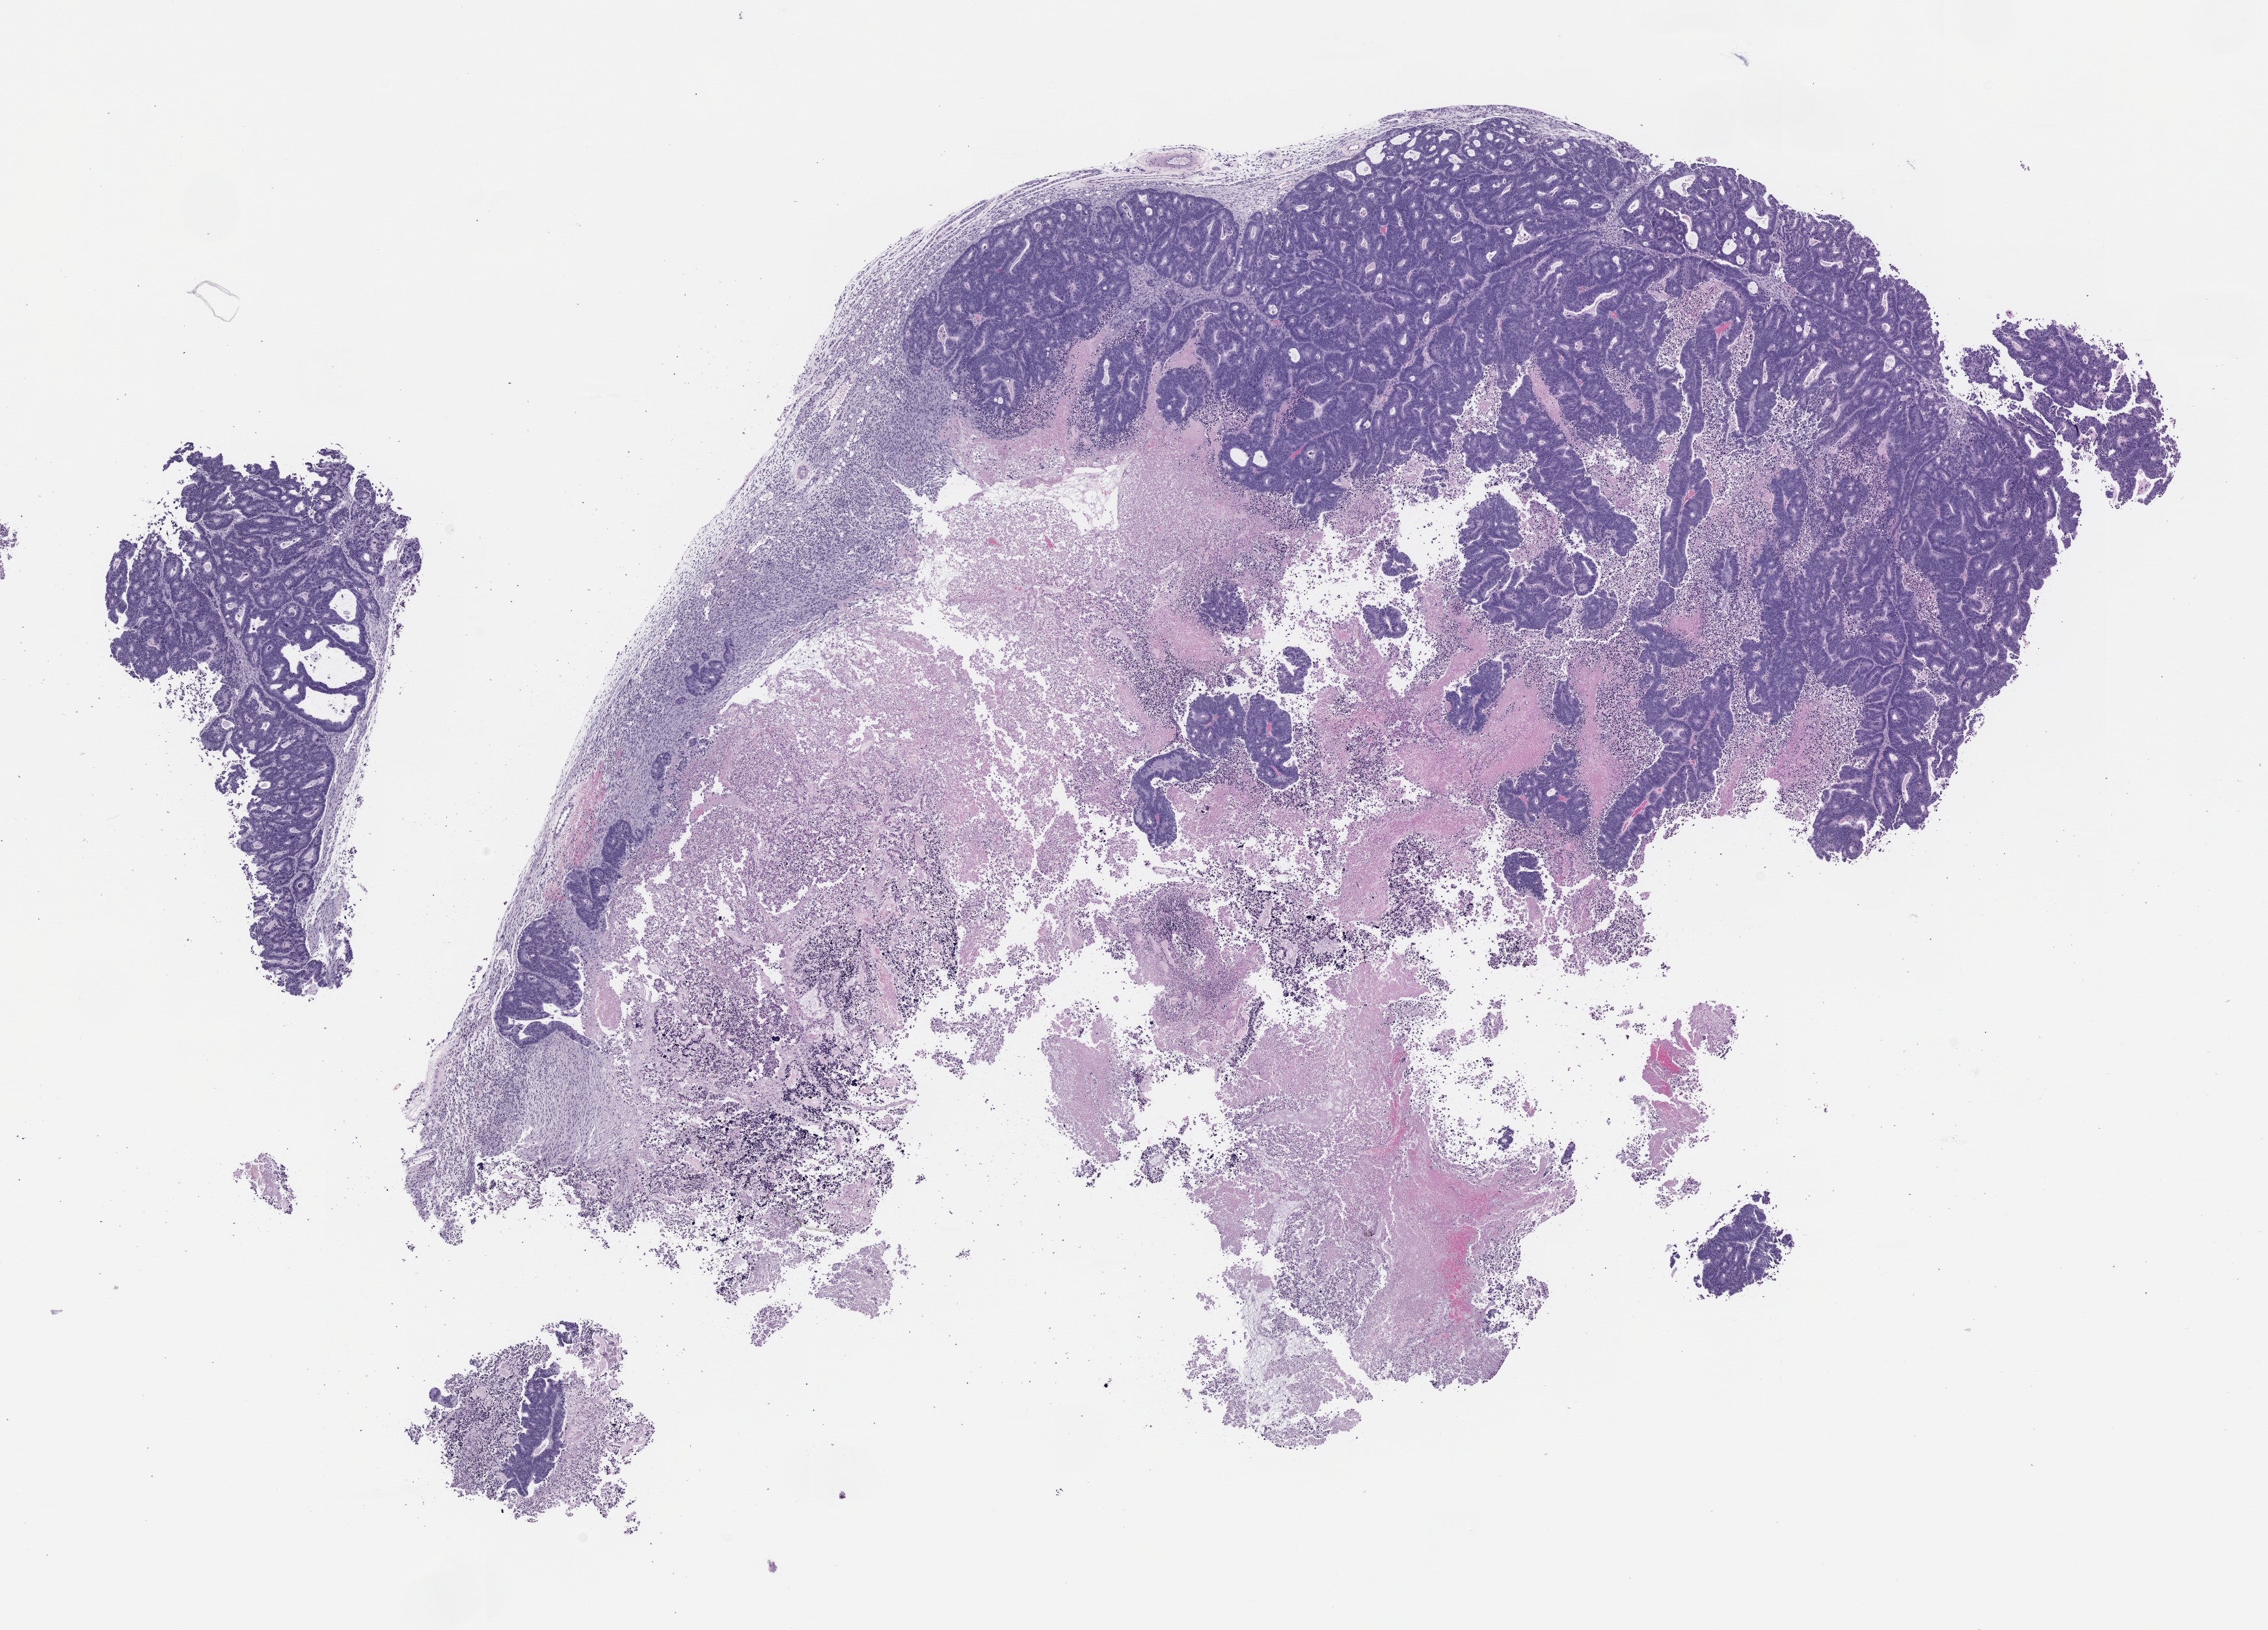
Whole-slide image, H&E: patient-derived xenograft (human tumor grown in a mouse), passage 1 — a low-resolution overview of the entire scanned area, about 14.0 x 10.1 mm, formalin-fixed paraffin-embedded section, tumor site category: rectum.
Originating patient diagnosis: Rectal Adenocarcinoma.